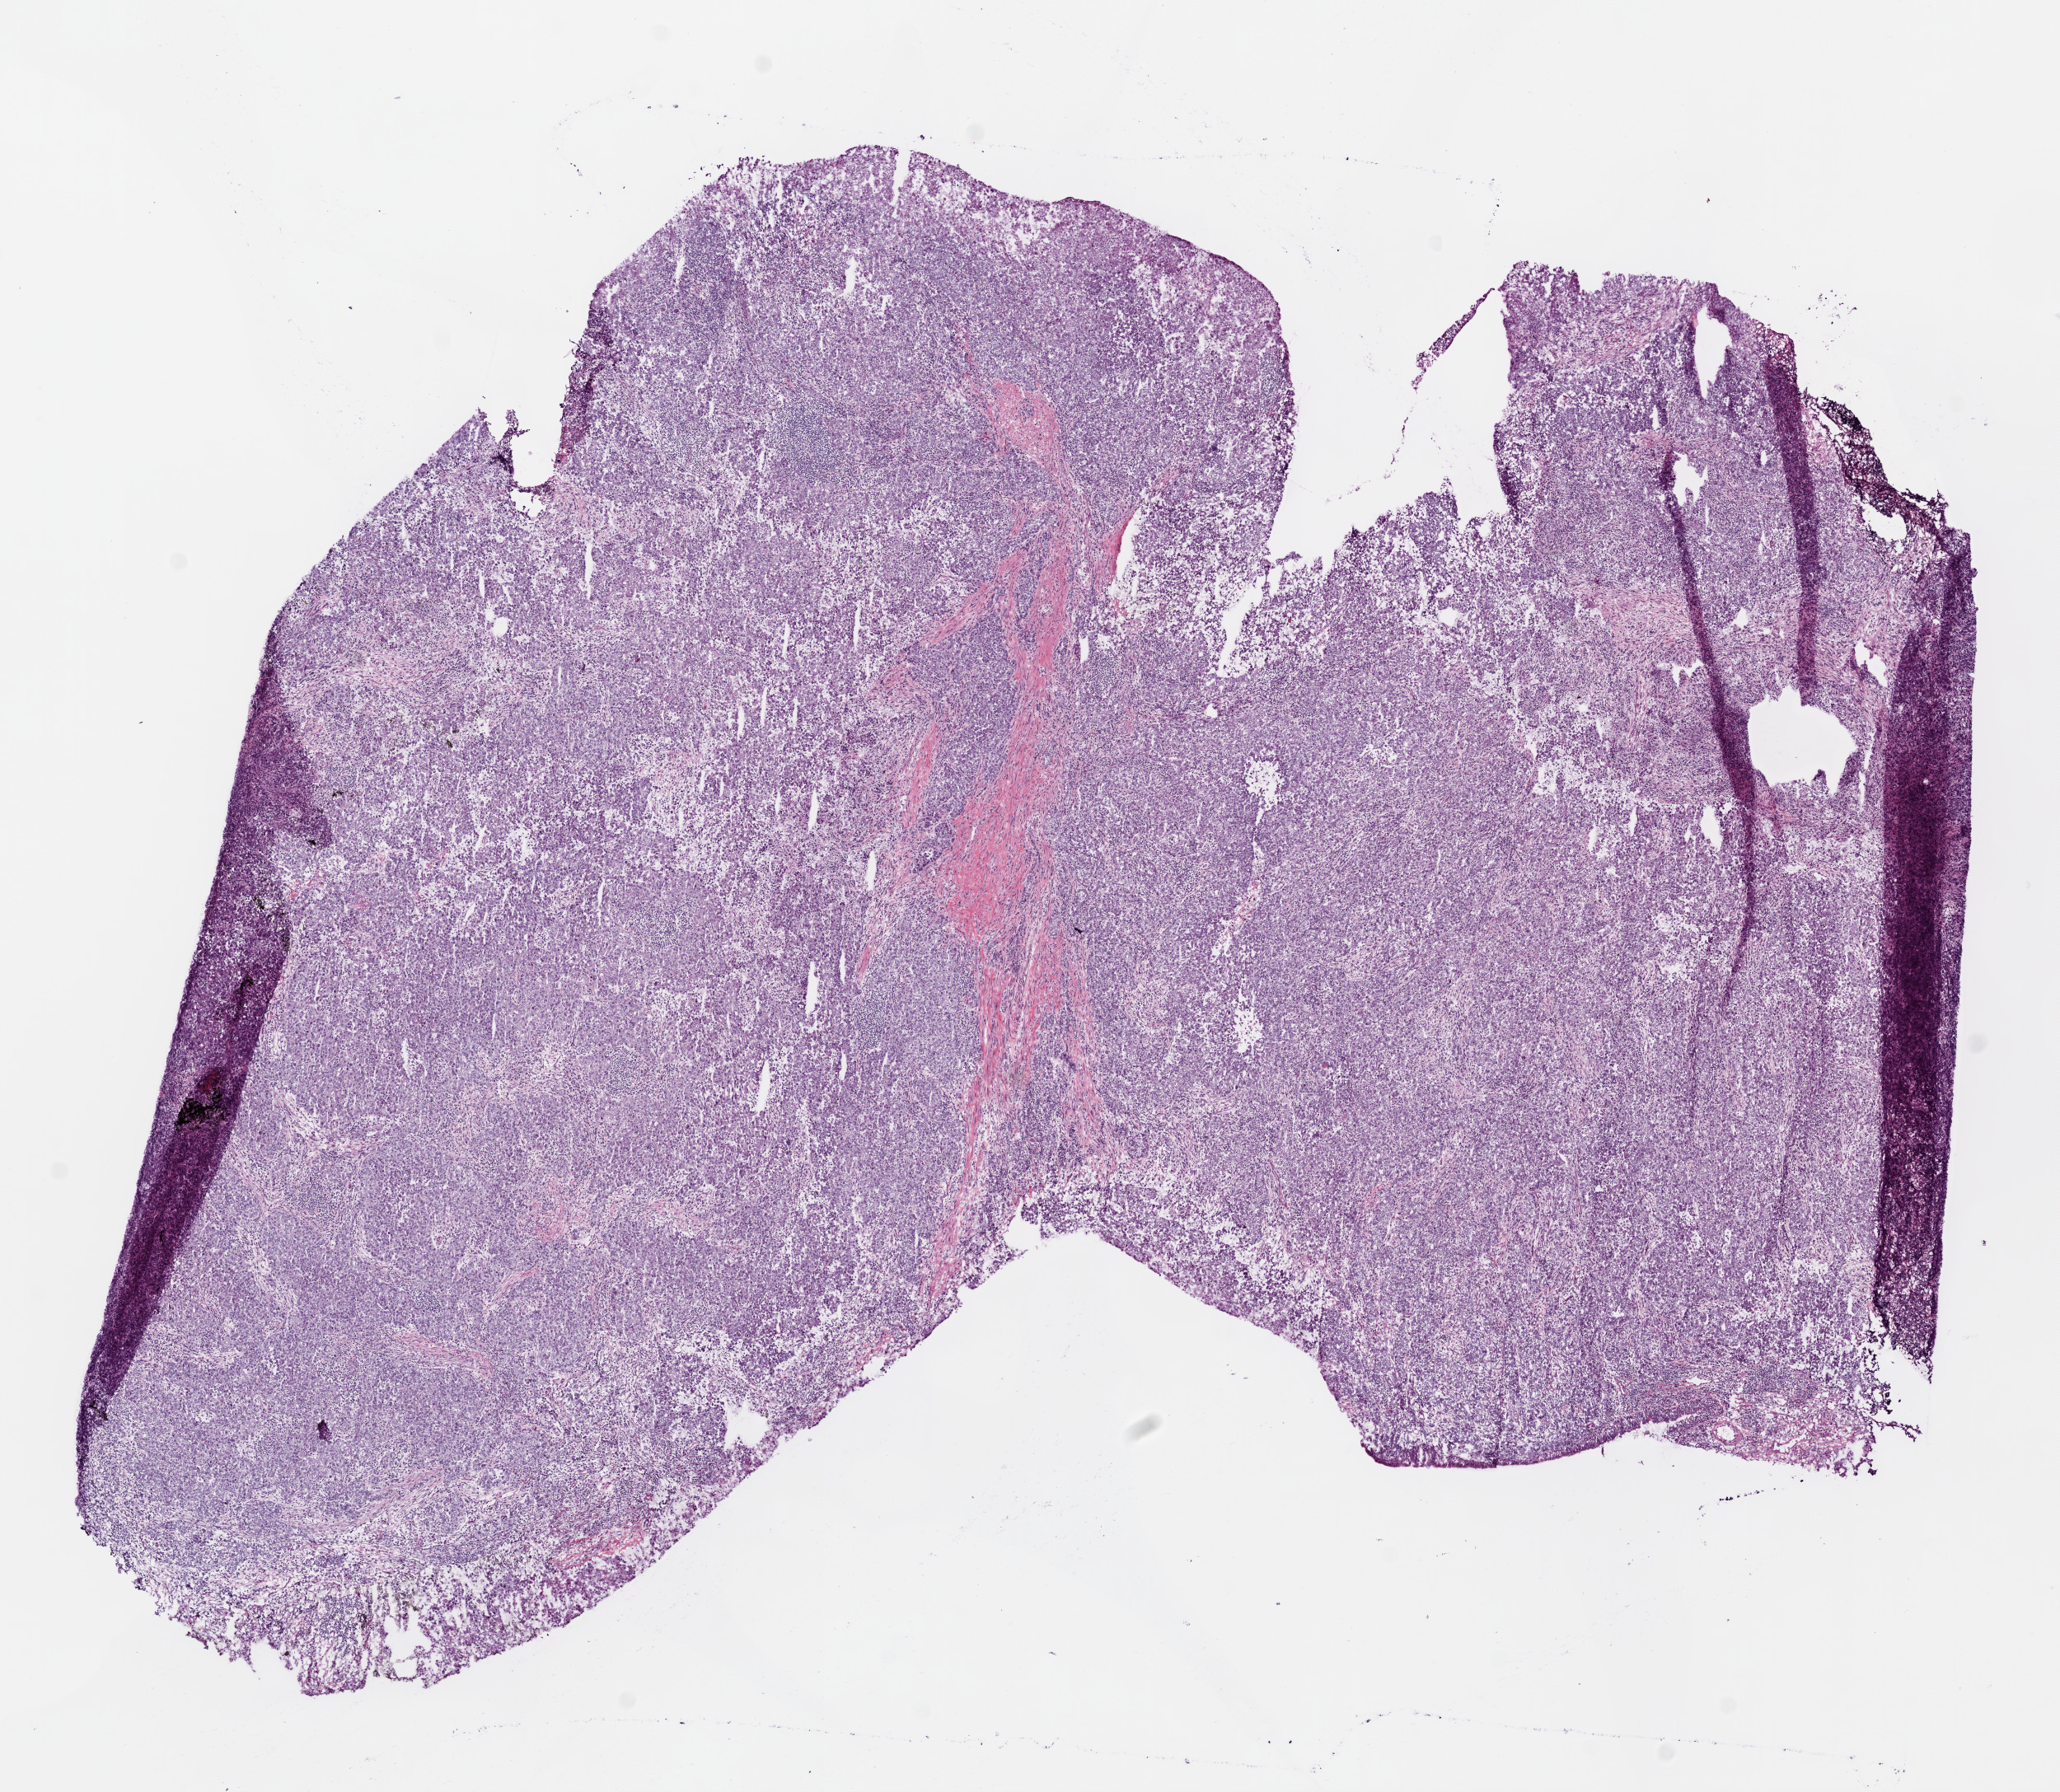
H&E-stained whole-slide image — low-resolution overview of the scanned area, about 10.0 x 8.7 mm (acquisition: 20x scan). Frozen section from the bottom of the tissue portion. Primary tumour sample from the lung. Patient: female, age at initial diagnosis 33 years. Slide review estimates, as recorded: tumour cells 93%, tumour nuclei 80%, stromal cells 5%, necrosis 2%. Infiltration values recorded for this section: lymphocyte infiltration 18%.
Pathologic diagnosis: Adenocarcinoma, NOS. AJCC pathologic stage: IB (6th edition).